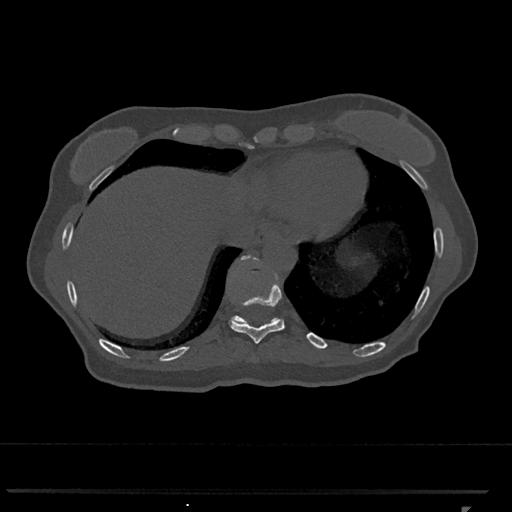
CT including the spine, one axial slice. Position 560 of 793 along the scan axis. Reconstruction kernel Br40s/3. Bone window (W 1800 / L 400 HU). 0.5 mm slice thickness. 512 × 512 image matrix, field of view 380 × 380 mm. Patient: female, 62 years. From the clinical record (not read from this slice): primary cancer: renal.
Annotated regions visible in this slice (semi-automatically segmented with operator editing):
- T10 vertebra: box from (x=229, y=269) to (x=285, y=344) px
- T11 vertebra: (x=231, y=255)–(x=280, y=324)